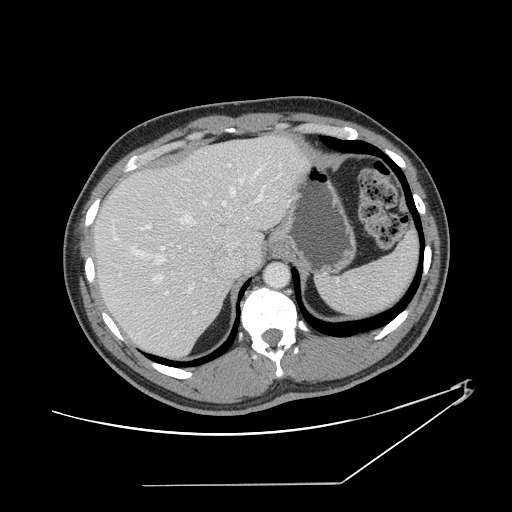
Contrast-enhanced abdominal CT, one axial slice. Slice 110 of 152 in the series (ordered by position). Reconstruction kernel STANDARD. Intravenous contrast given. Soft-tissue window (W 400 / L 40 HU). 512 × 512 image matrix. Male patient, age 45 years. Case-level facts recorded for this patient, not image findings: diagnosis: colorectal cancer liver metastases, imaged before liver resection; multiple liver metastases: no; largest metastasis: 1 cm; chemotherapy before resection: yes.
Outlined on this slice (expert manual segmentation):
- hepatic veins: bounding box [x1, y1, x2, y2] px = [111, 156, 270, 293]
- liver: [95, 136, 301, 360]
- planned liver remnant (the part of the liver to remain after resection): [95, 157, 234, 360]
- portal vein (with intrahepatic branches): [160, 165, 281, 315]